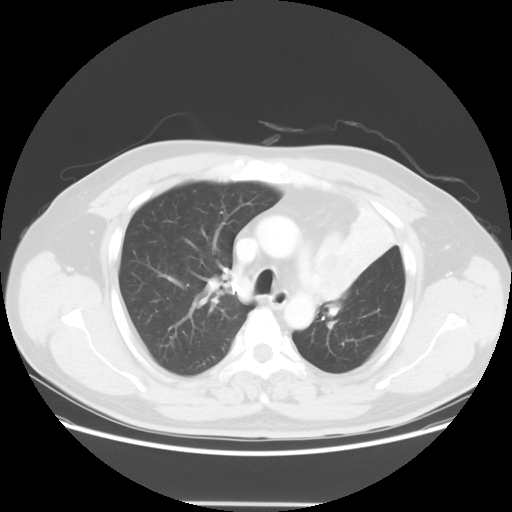
Chest CT, one axial slice; reconstruction kernel STANDARD; lung window (W 1500 / L -600 HU); 5 mm slice thickness; 512 × 512 image matrix, field of view 403 × 403 mm. Patient: male, 49 years. Case-level facts recorded for this patient, not image findings: clinical TNM (as recorded): T3 N3 M1c.
Outlined on this slice (rectangle marked by the reading radiologist):
- lung tumour (recorded histology: squamous cell carcinoma): bounding box [x1, y1, x2, y2] px = [301, 236, 356, 312]